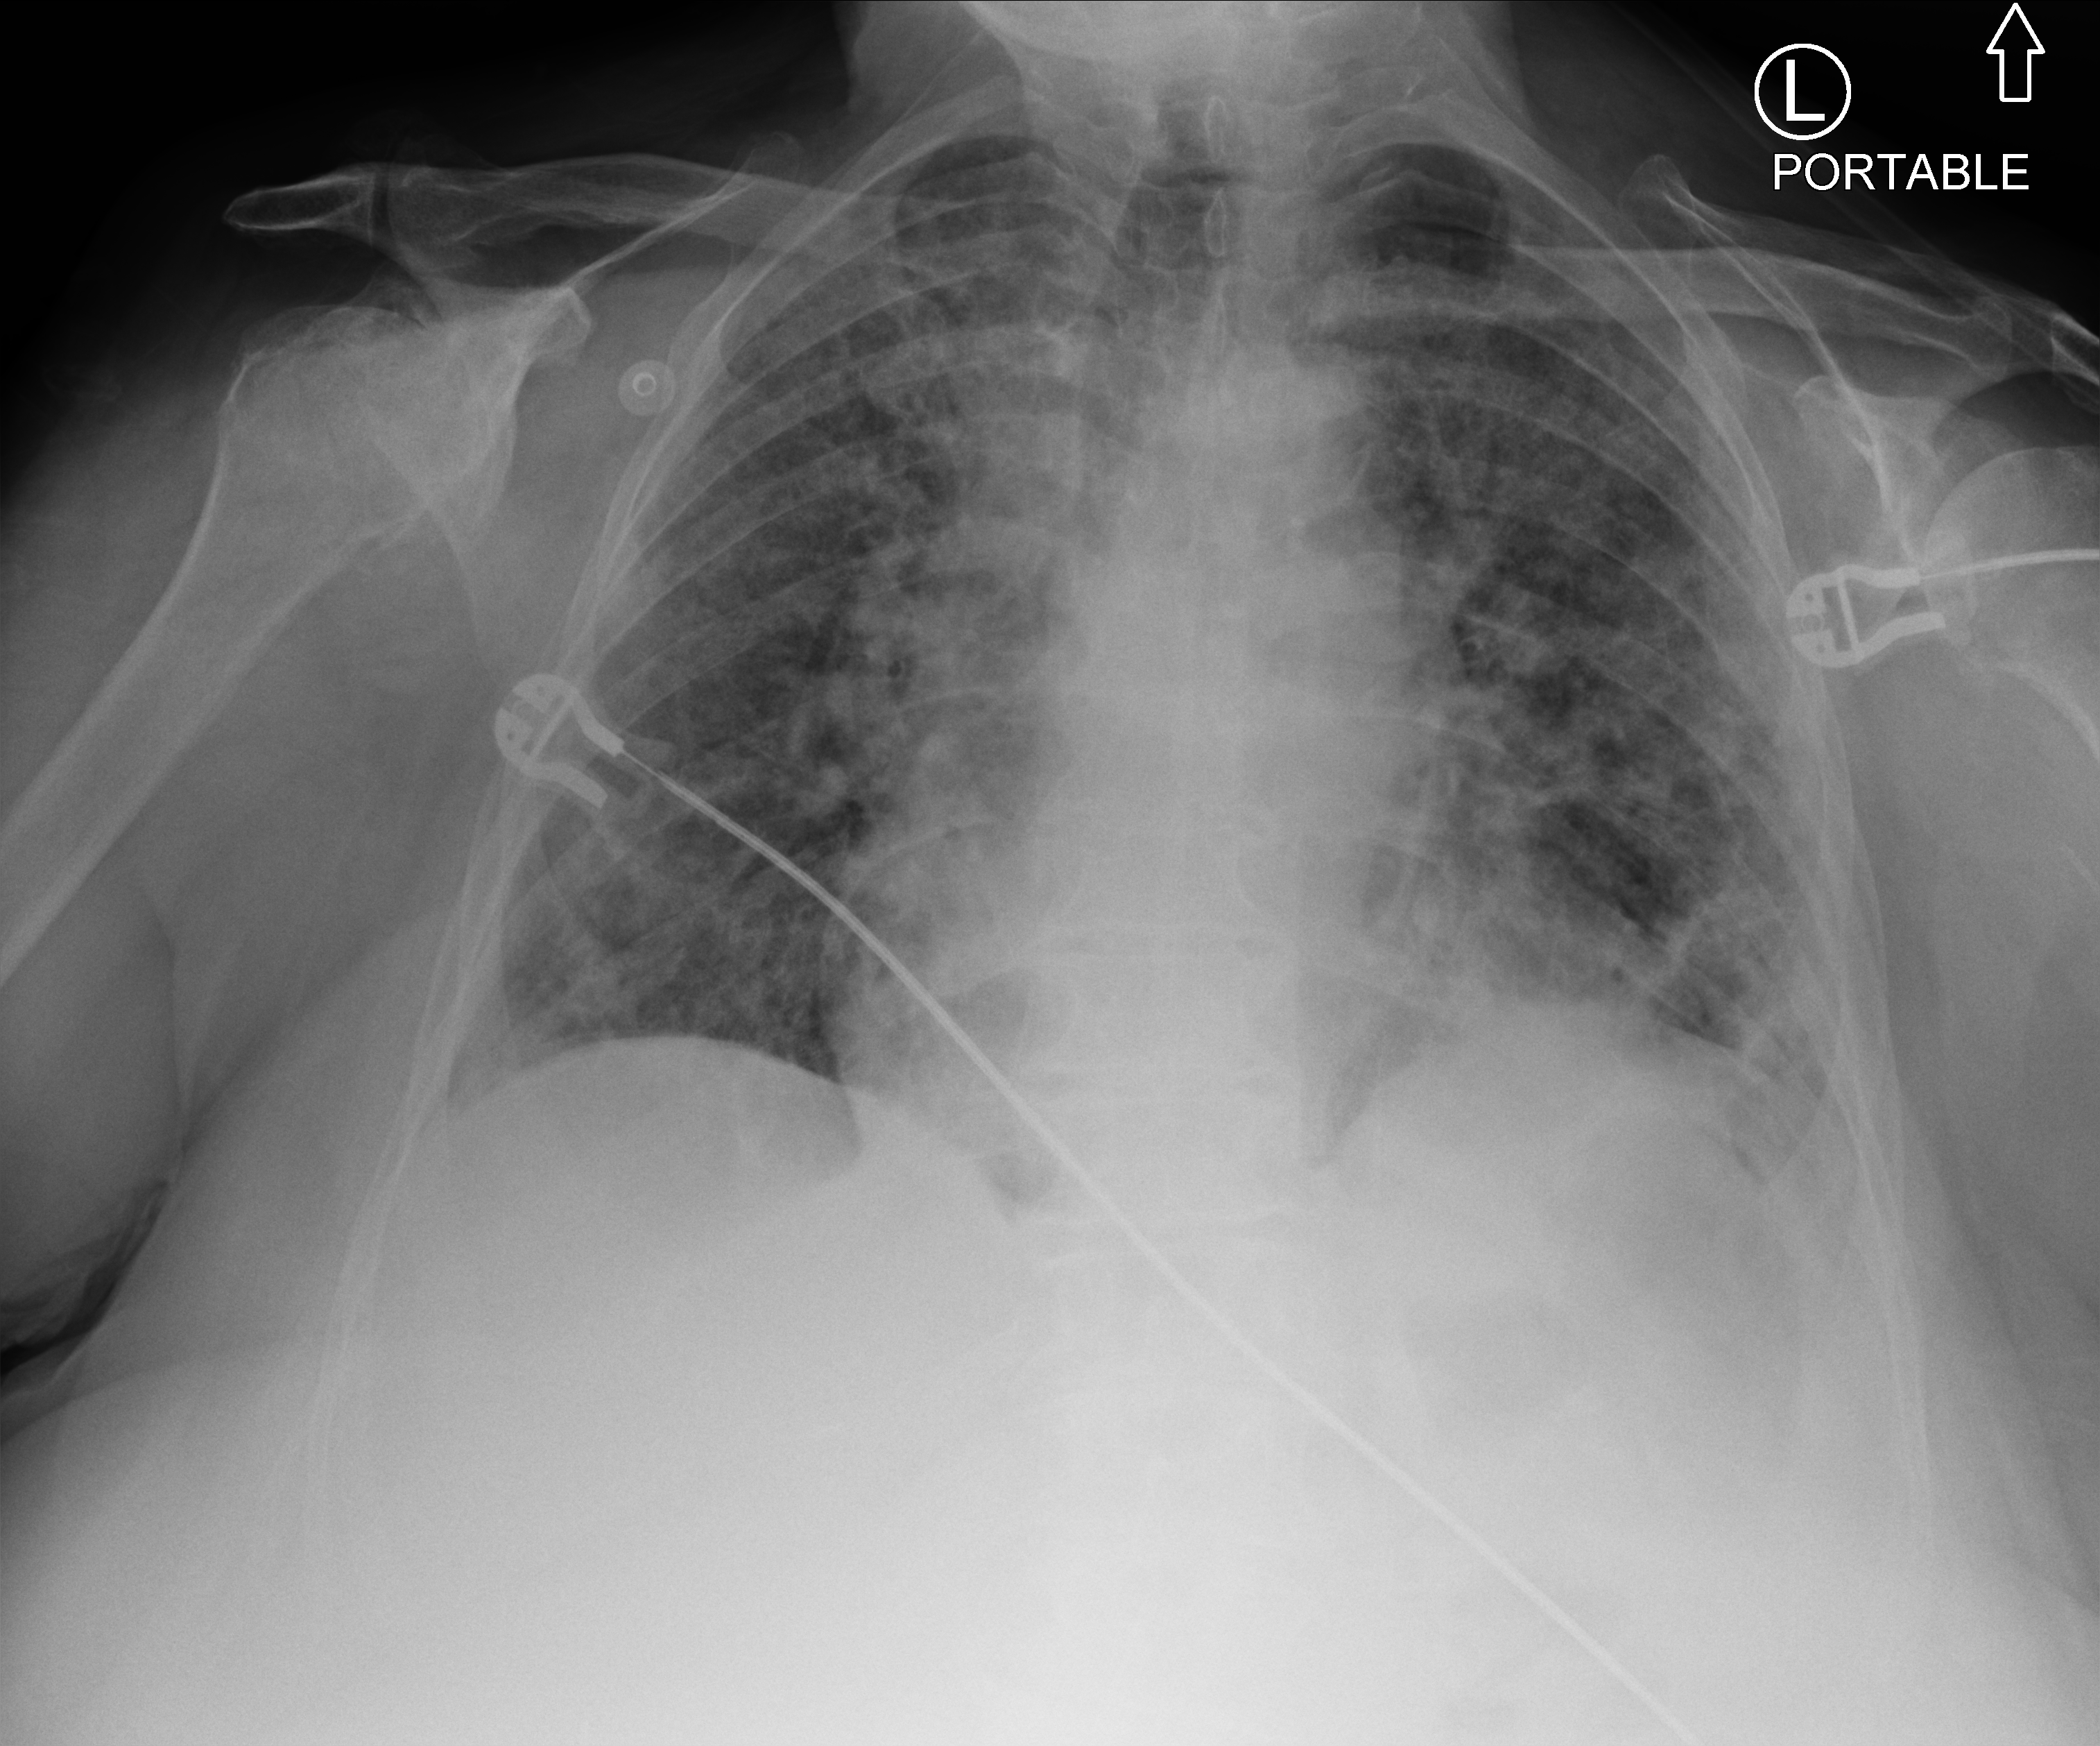
Portable chest radiograph; anteroposterior (AP) projection. Female patient hospitalised with COVID-19, age 60–74 years.
Admission-level facts for this patient (not findings on this image; timing relative to this image not recorded):
- admitted to intensive care during this hospital stay: no